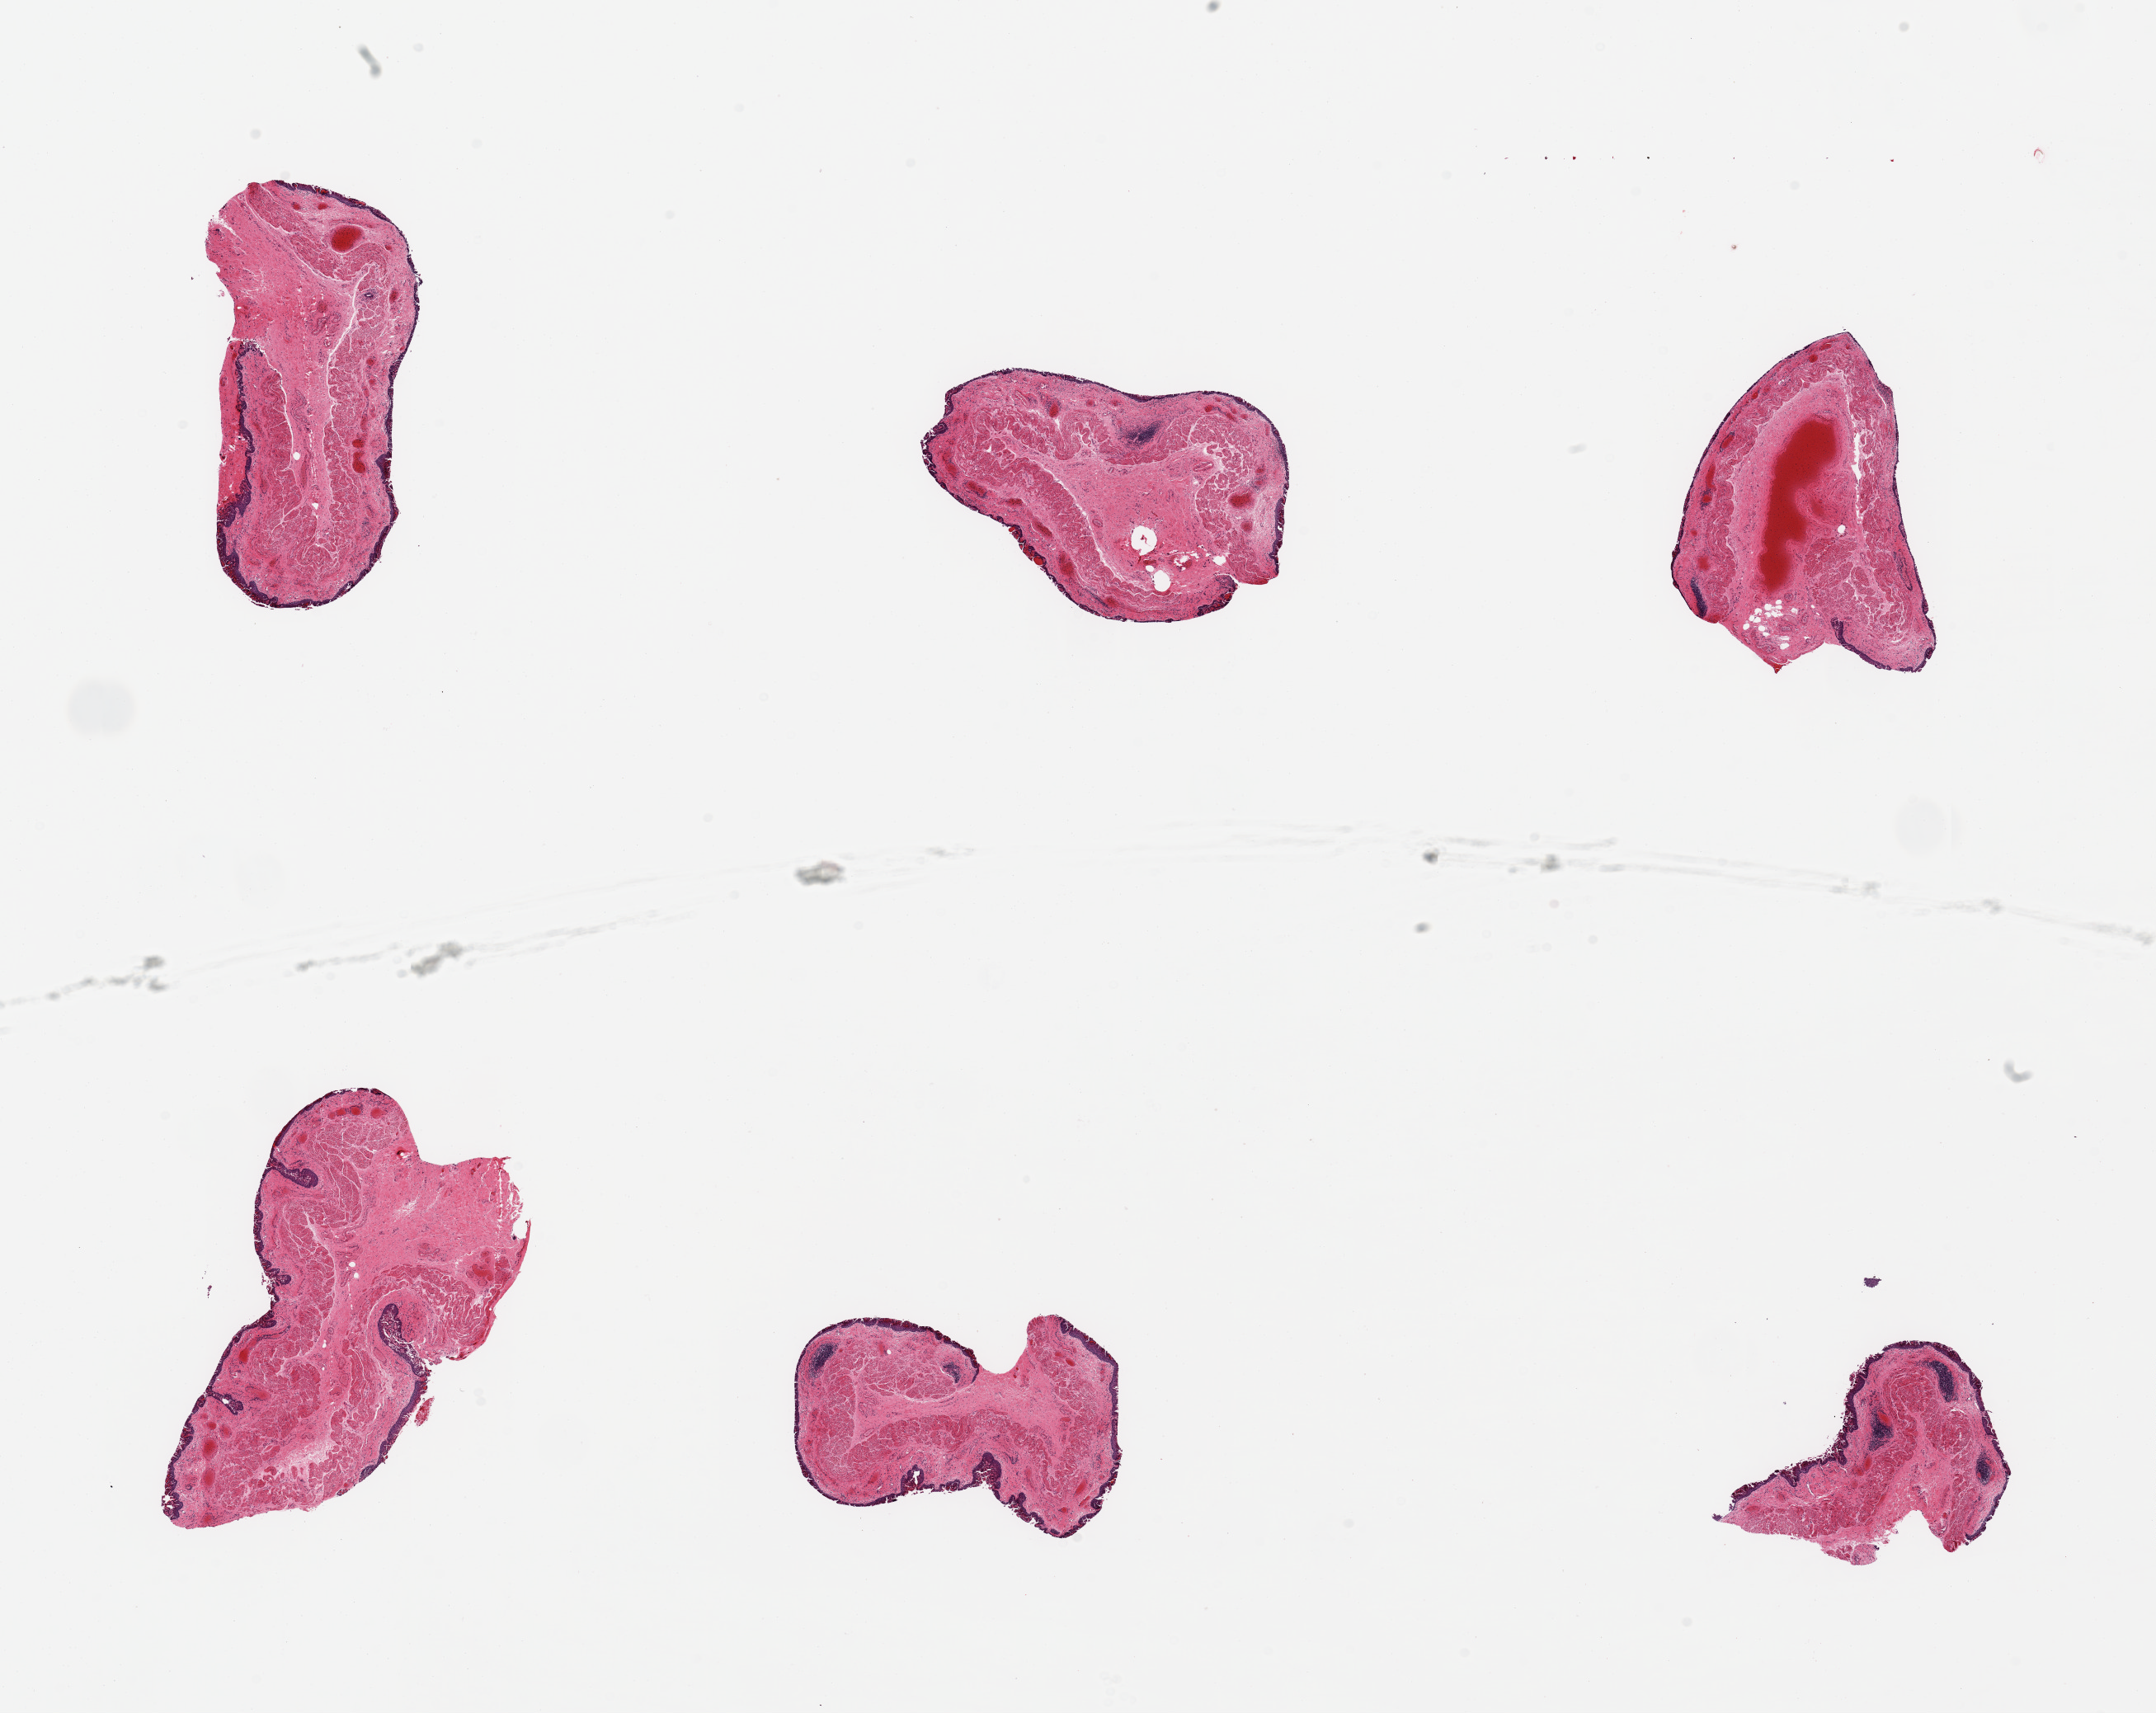
Hematoxylin and eosin (H&E) whole-slide image, shown as a low-resolution overview of the whole scanned area (about 20.7 x 16.4 mm); PAXgene-fixed paraffin-embedded (PFPE) section; section of esophageal mucous membrane (target tissue); tissue donor sample. Donor sex: male.
Pathologist's review note for this sample: 6 pieces; largely desquamated squamous lining; better preserved prominent muscularis mucosae.